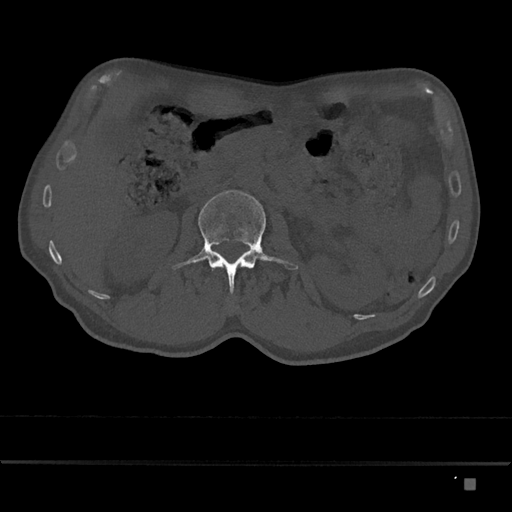
CT including the spine, one axial slice; slice 478 of 797 in the series (ordered by position); reconstruction kernel Br40s/3; 120 kVp; bone window (W 1800 / L 400 HU); 0.5 mm slice thickness; 512 × 512 image matrix, field of view 390 × 390 mm. Male patient, age 72 years. From the clinical record (not read from this slice): primary cancer: prostate.
Outlined on this slice (semi-automatic segmentation, software-assisted and operator-edited):
- L2 vertebra: box from (x=172, y=190) to (x=298, y=294) px